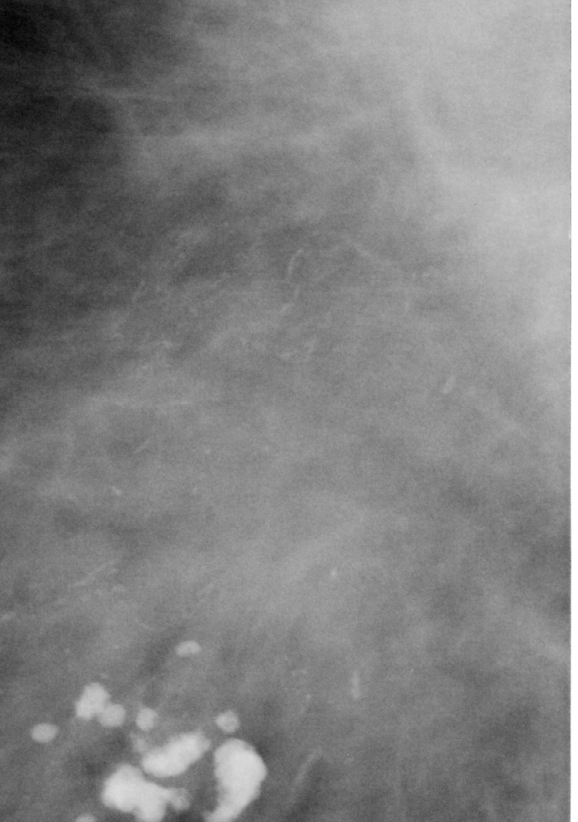
Region of interest cut from a scanned film mammogram (one marked finding), right breast, MLO view.
- Marked abnormality: mass, shape irregular / architectural distortion, margins ill defined / spiculated; BI-RADS assessment category 5; subtlety rating 5 on a 1 (subtle) to 5 (obvious) scale; pathology result (as recorded, not read from the image): malignant.